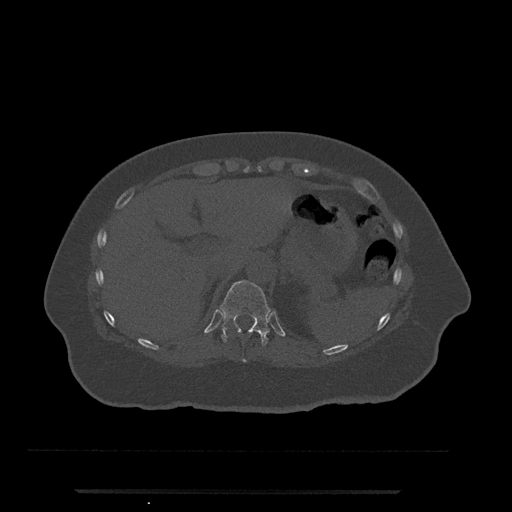
CT including the spine, one axial slice; position 244 of 797 along the scan axis; reconstruction kernel Br40s/3; 120 kVp; bone window (W 1800 / L 400 HU); 0.5 mm slice thickness; 512 × 512 image matrix. Patient: female, 51 years. Case-level facts recorded for this patient, not image findings: primary cancer: neuro.
Outlined on this slice (semi-automatically segmented with operator editing):
- T10 vertebra: bounding box [x1, y1, x2, y2] px = [242, 359, 246, 362]
- T11 vertebra: [220, 280, 271, 346]